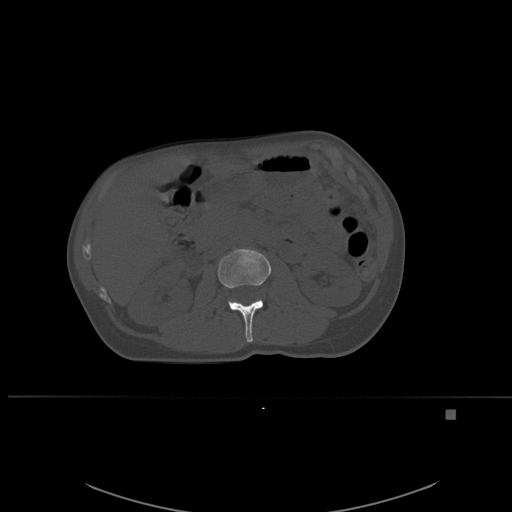
CT including the spine, one axial slice. Slice 232 of 537 in the series (ordered by position). Bone window (W 1800 / L 400 HU). 1.5 mm slice thickness. 512 × 512 image matrix, field of view 440 × 440 mm. Female patient, age 45 years. Case-level facts recorded for this patient, not image findings: primary cancer: lung.
Structures marked on this image (semi-automatically segmented with operator editing):
- L2 vertebra: bounding box <218,249,272,342> (left, top, right, bottom; pixels)